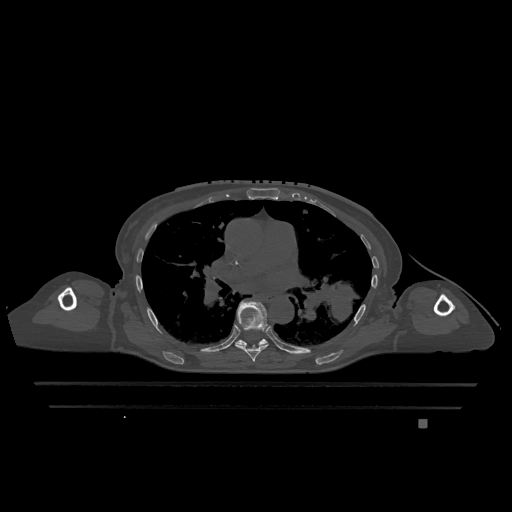
CT including the spine, one axial slice; position 770 of 1317 along the scan axis; bone window (W 1800 / L 400 HU); 0.5 mm slice thickness; 512 × 512 image matrix. Female patient, age 74 years. Case-level facts recorded for this patient, not image findings: primary cancer: lung; vertebrae with lytic lesions (as recorded): T1, T4, T5, T6, L4, L5.
Outlined on this slice (semi-automatically segmented with operator editing):
- T6 vertebra: bounding box [x1, y1, x2, y2] px = [235, 301, 269, 362]
- T7 vertebra: [235, 339, 268, 346]